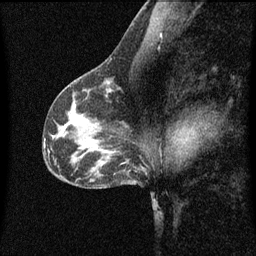
Breast MRI (dynamic contrast-enhanced), one sagittal slice. Dynamic contrast-enhanced series, image 2 of 3 at this slice position (ordered by acquisition). 1.5 T. TE 4.2 ms, TR 8.4 ms. 256 × 256 image matrix. Female patient, age 41 years.
Annotated regions visible in this slice (semi-automatic segmentation, software-assisted and operator-edited):
- analysis volume of interest (the breast-tissue region the enhancement analysis was run in; not a lesion): bounding box (x1, y1, x2, y2) in pixels: (94, 72, 119, 97)
- tumour enhancement mask (voxels above the 70 % enhancement threshold inside the analysis volume of interest): (106, 80, 119, 89)